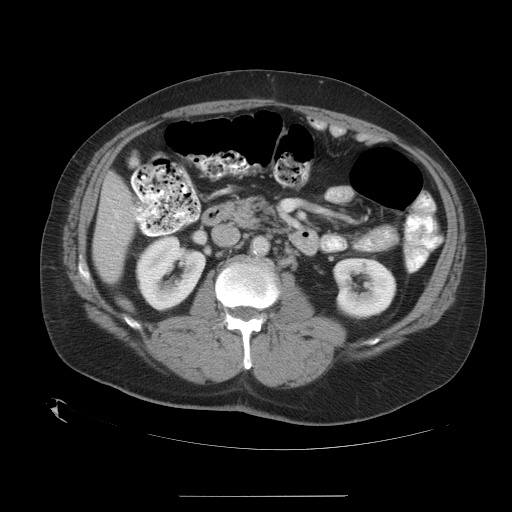
Contrast-enhanced abdominal CT, one axial slice; slice 11 of 35 in the series (ordered by position); intravenous contrast given; soft-tissue window (W 400 / L 40 HU); 7.5 mm slice thickness; 512 × 512 image matrix, field of view 450 × 450 mm. Male patient, age 67 years. Case-level facts recorded for this patient, not image findings: diagnosis: colorectal cancer liver metastases, imaged before liver resection; multiple liver metastases: no; largest metastasis: 2.3 cm; disease in both lobes: no.
Annotated regions visible in this slice (outlined manually by an expert reader):
- liver: box from (x=94, y=177) to (x=135, y=279) px
- planned liver remnant (the part of the liver to remain after resection): (x=94, y=177)–(x=135, y=279)
- portal vein (with intrahepatic branches): (x=111, y=215)–(x=137, y=229)